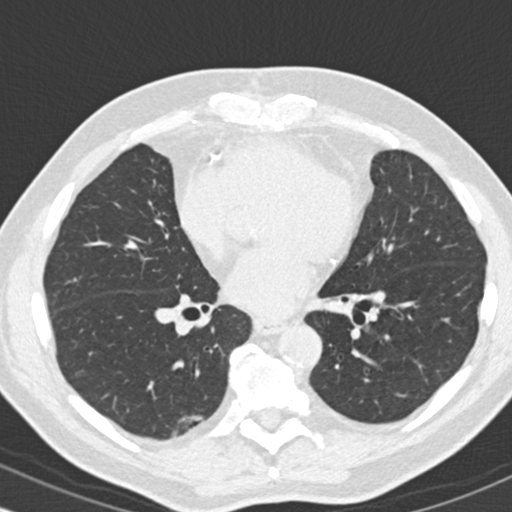
Axial slice from a low-dose chest CT screening exam; second screening round (one year after baseline); lung window (W 1500 / L -600 HU); slice 101 of 180 in the series; 512 × 512 image matrix, field of view 318 × 318 mm. Male participant, aged 68 years at enrolment.
- Expert reader's lesion annotation, bounding box [x1, y1, x2, y2] px = [165, 402, 217, 446].
- The screening reader recorded 2 non-calcified nodules or masses ≥4 mm on this exam; which of them this box marks is not recorded.
- Later outcome: lung cancer diagnosed 476 days after this screen — adenosquamous carcinoma, right lower lobe, moderately differentiated (G2), stage IB (AJCC 6th edition), 31 mm at pathology.